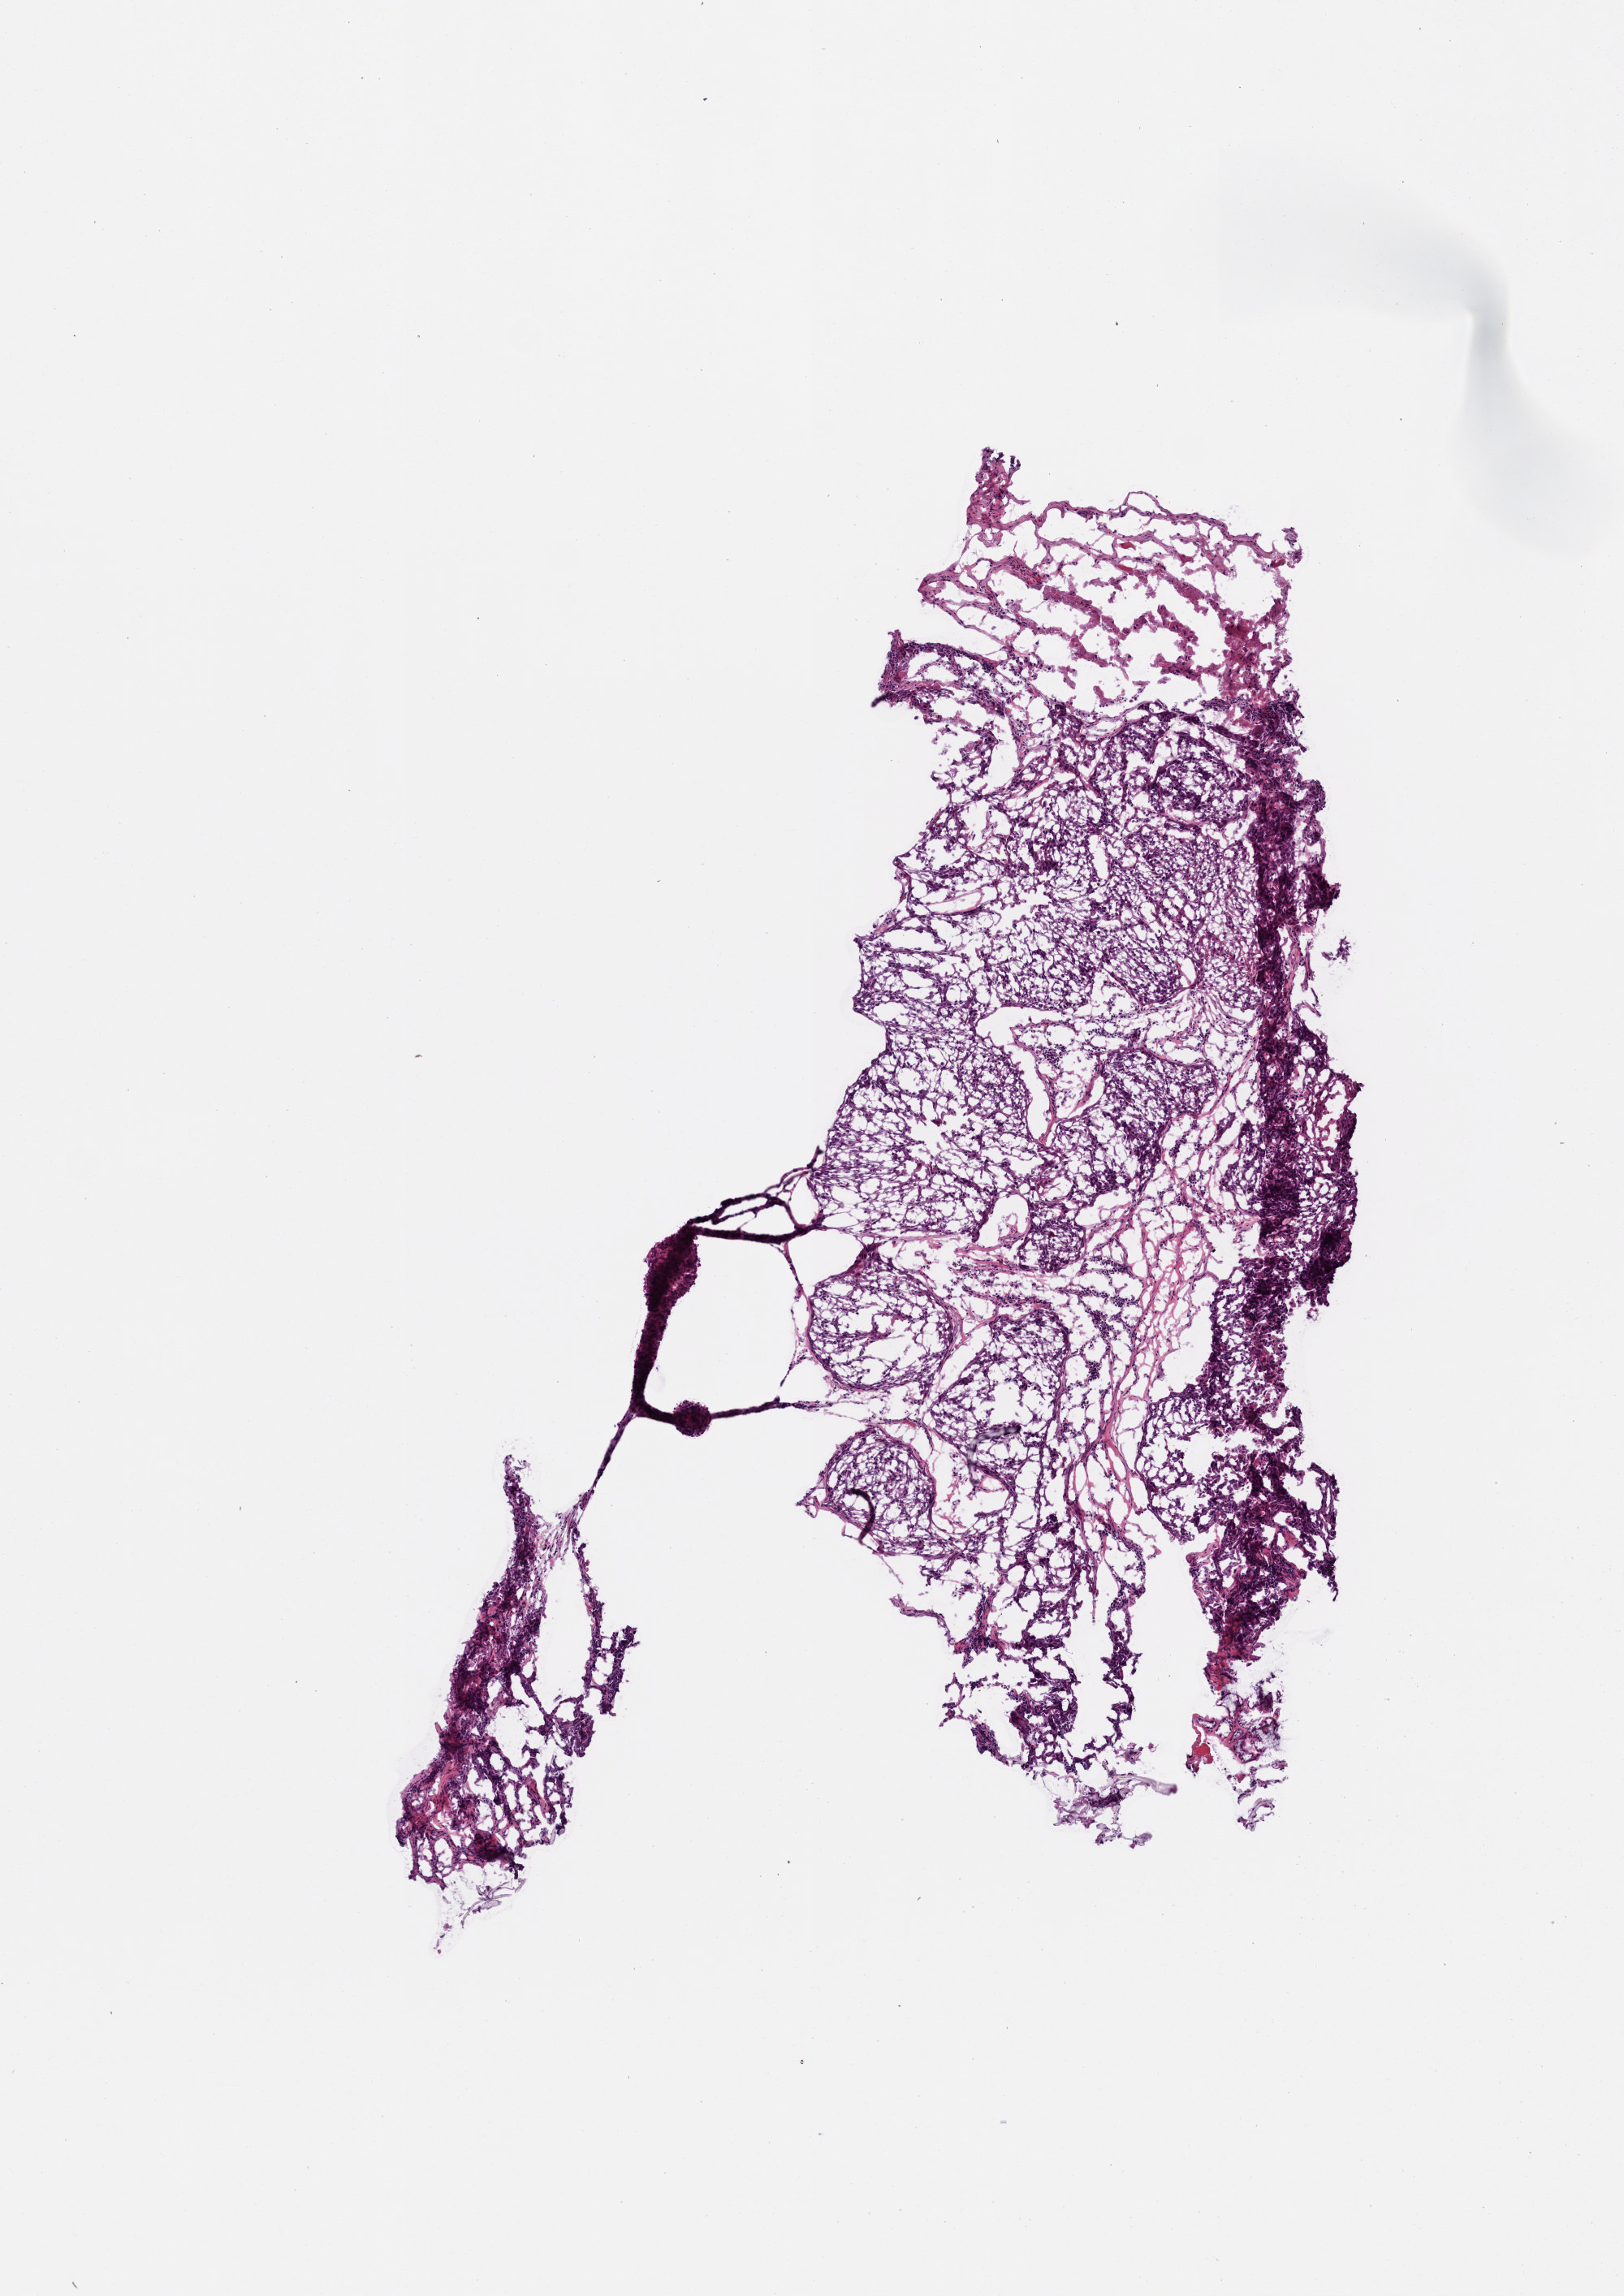
H&E-stained whole-slide image, a low-resolution overview of the entire scanned area, about 4.0 x 5.7 mm. Frozen section from the top of the tissue portion. Primary tumour sample from the head and neck. Female, age 56 years at initial diagnosis. Histologic grade: G3 (poorly differentiated). Pathologist review of this section (percent, as recorded): tumour cells 90%, tumour nuclei 80%, normal cells 0%, stromal cells 10%, necrosis 0%.
Laterality: left. AJCC pathologic stage: IVA (6th edition). Pathologic diagnosis: Squamous cell carcinoma, NOS.